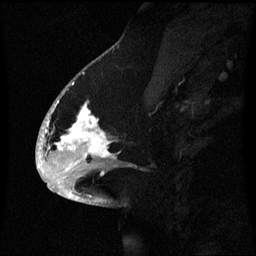
Breast MRI (dynamic contrast-enhanced), one sagittal slice; position 28 of 60 along the scan axis; dynamic contrast-enhanced series, image 2 of 3 at this slice position (ordered by acquisition); 1.5 T; TE 4.2 ms, TR 8.4 ms; 2.1 mm slice thickness; 256 × 256 image matrix, field of view 220 × 220 mm. Female patient, age 53 years. From the clinical record (not read from this slice): setting: breast cancer imaged before/during neoadjuvant chemotherapy; receptor status: HR-positive, HER2-negative.
Structures marked on this image (semi-automatically segmented with operator editing):
- analysis volume of interest (the breast-tissue region the enhancement analysis was run in; not a lesion): bounding box (x1, y1, x2, y2) in pixels: (52, 90, 131, 171)
- tumour enhancement mask (voxels above the 70 % enhancement threshold inside the analysis volume of interest): (52, 100, 112, 159)